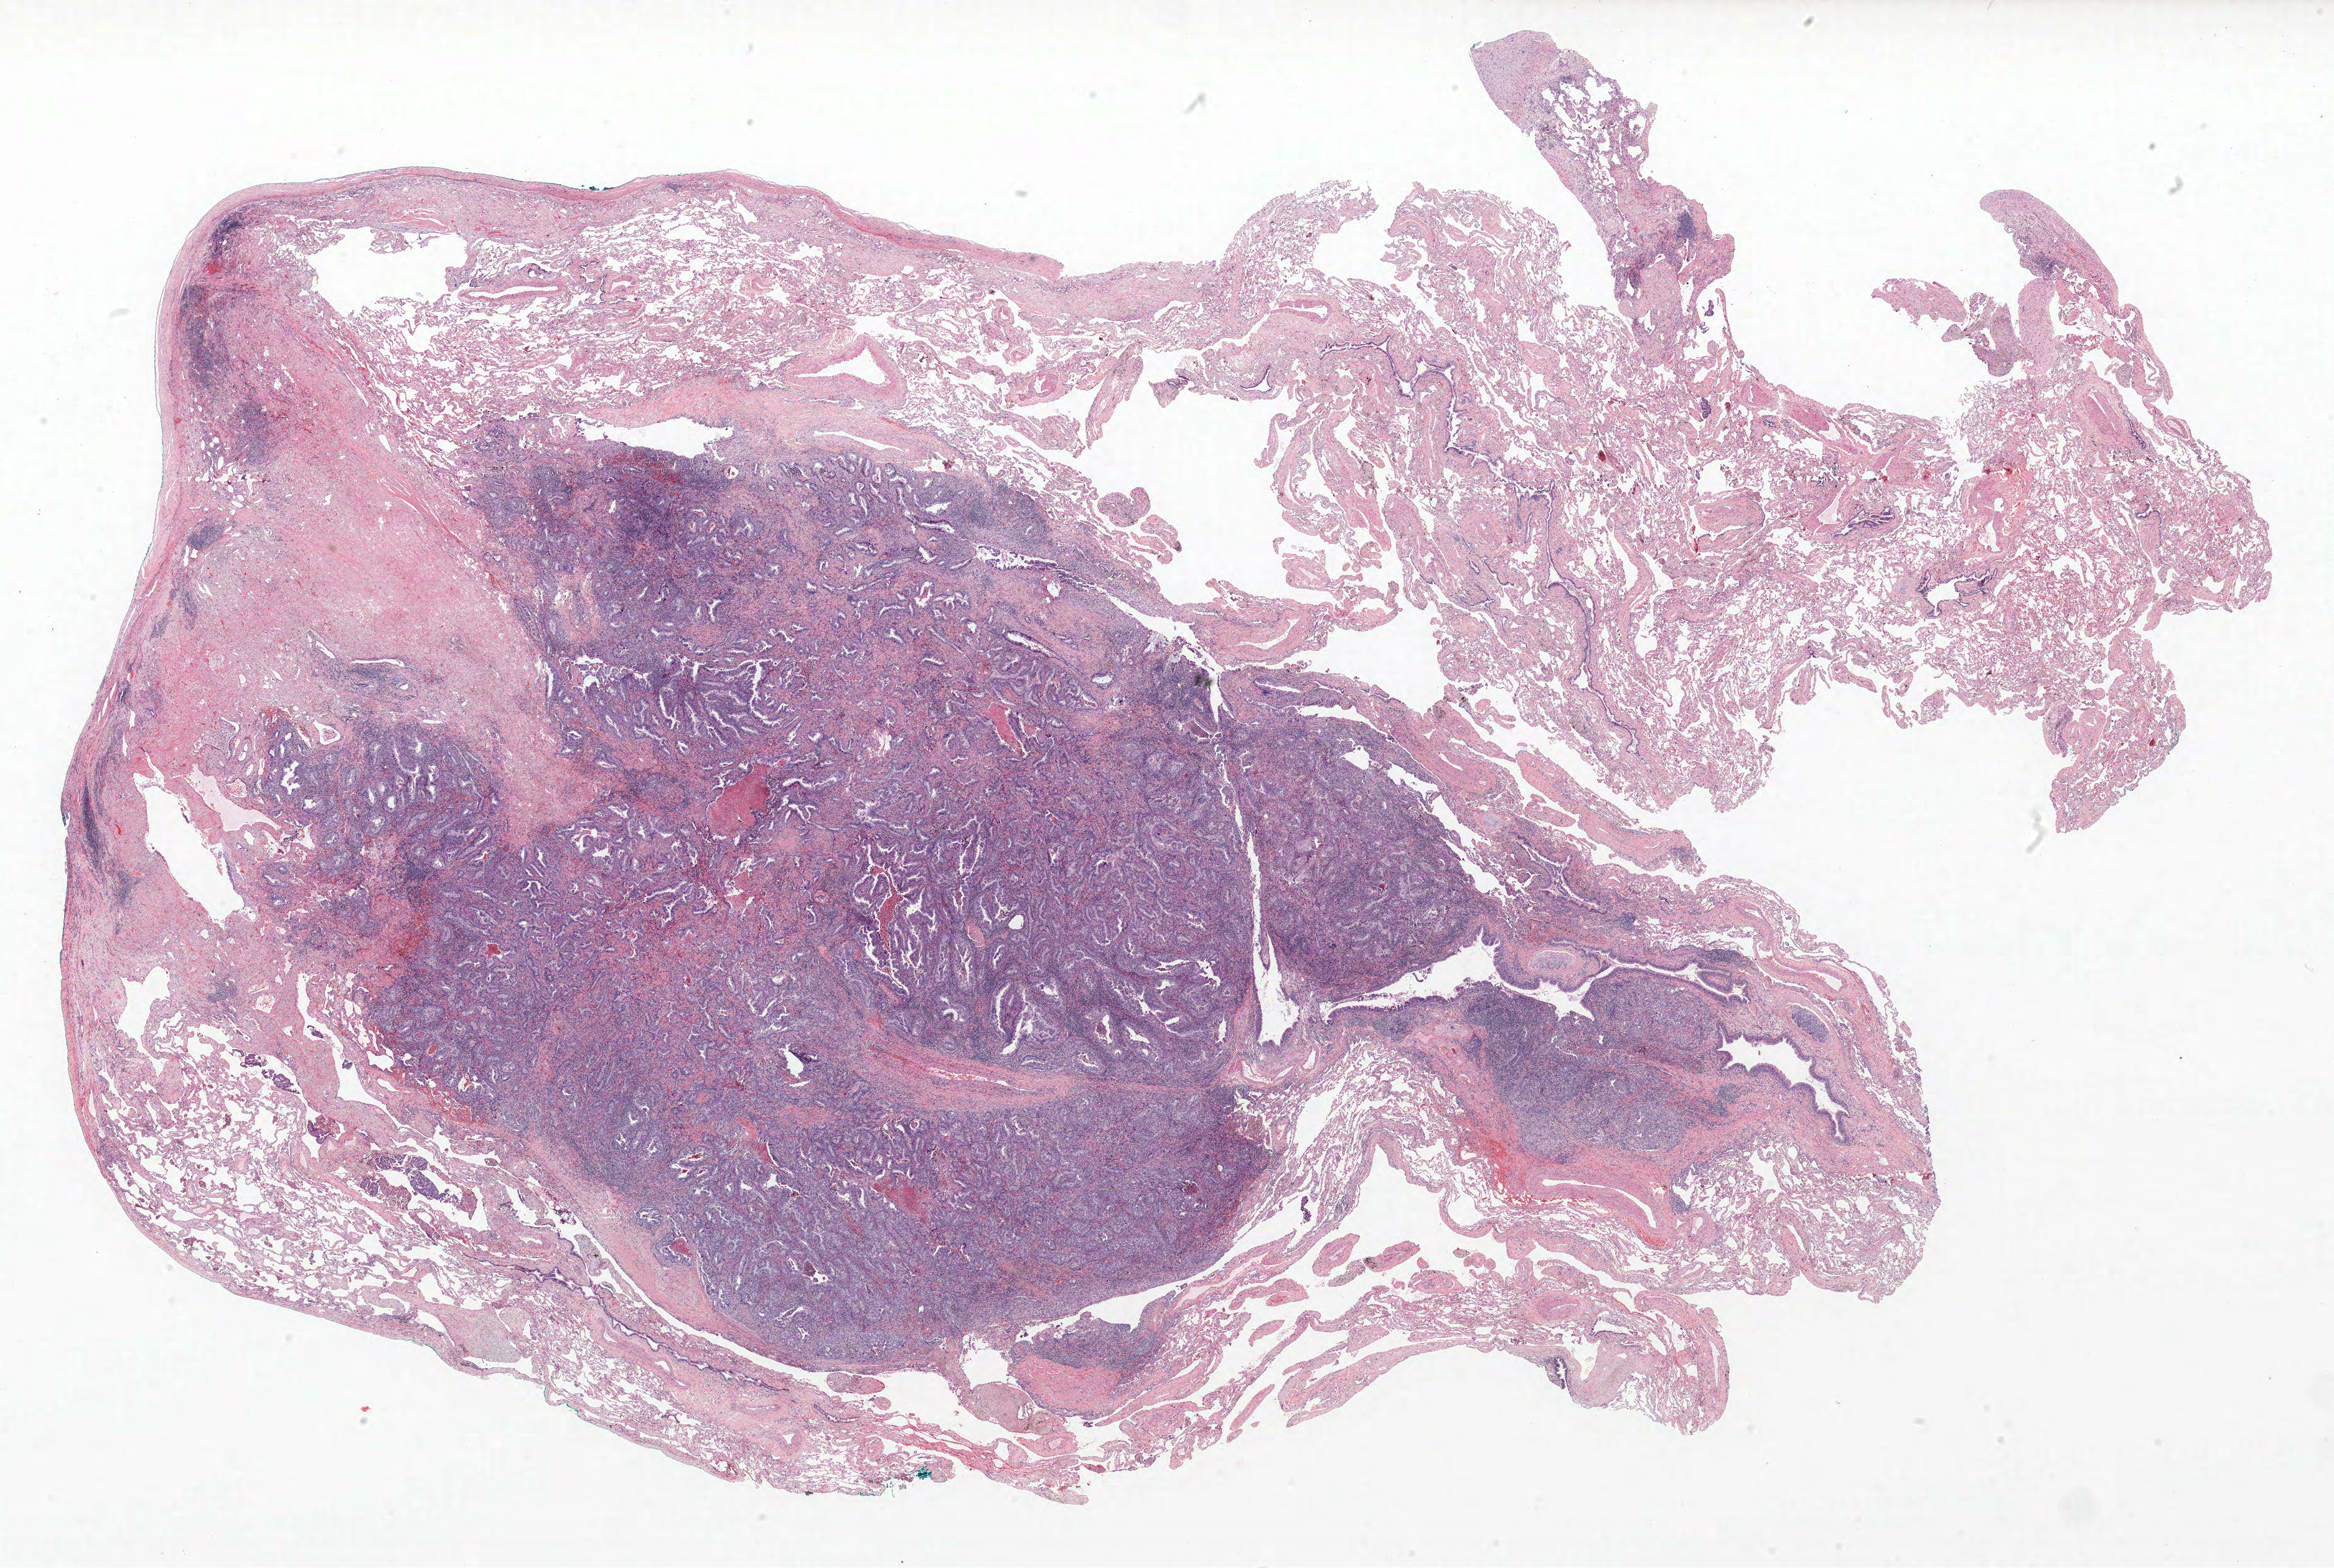
Whole-slide histology image, H&E, whole scanned area (about 30.0 x 20.2 mm, slide scanned at 40x) shown as a low-resolution overview, FFPE section, lung tissue. Male patient, aged 63 at enrolment. Current smoker at enrolment. Grade: moderately differentiated (G2).
Primary tumour location (clinical record): right upper lobe. Participant's lung-cancer diagnosis: Adenocarcinoma, NOS. Tumour size (pathology): 17 mm. Stage (AJCC 6th edition): IIIB.